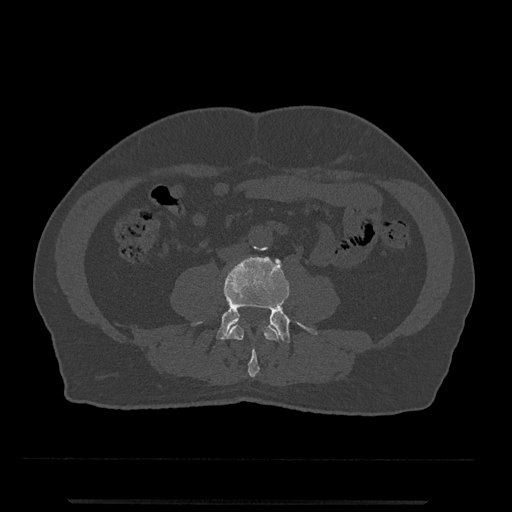
CT including the spine, one axial slice; position 161 of 797 along the scan axis; reconstruction kernel Br40s/3; bone window (W 1800 / L 400 HU); 0.5 mm slice thickness; 512 × 512 image matrix, field of view 419 × 419 mm. Male patient, age 63 years. From the clinical record (not read from this slice): primary cancer: prostate.
Annotated regions visible in this slice (semi-automatically segmented with operator editing):
- L3 vertebra: box from (x=226, y=324) to (x=280, y=377) px
- L4 vertebra: (x=191, y=257)–(x=317, y=343)